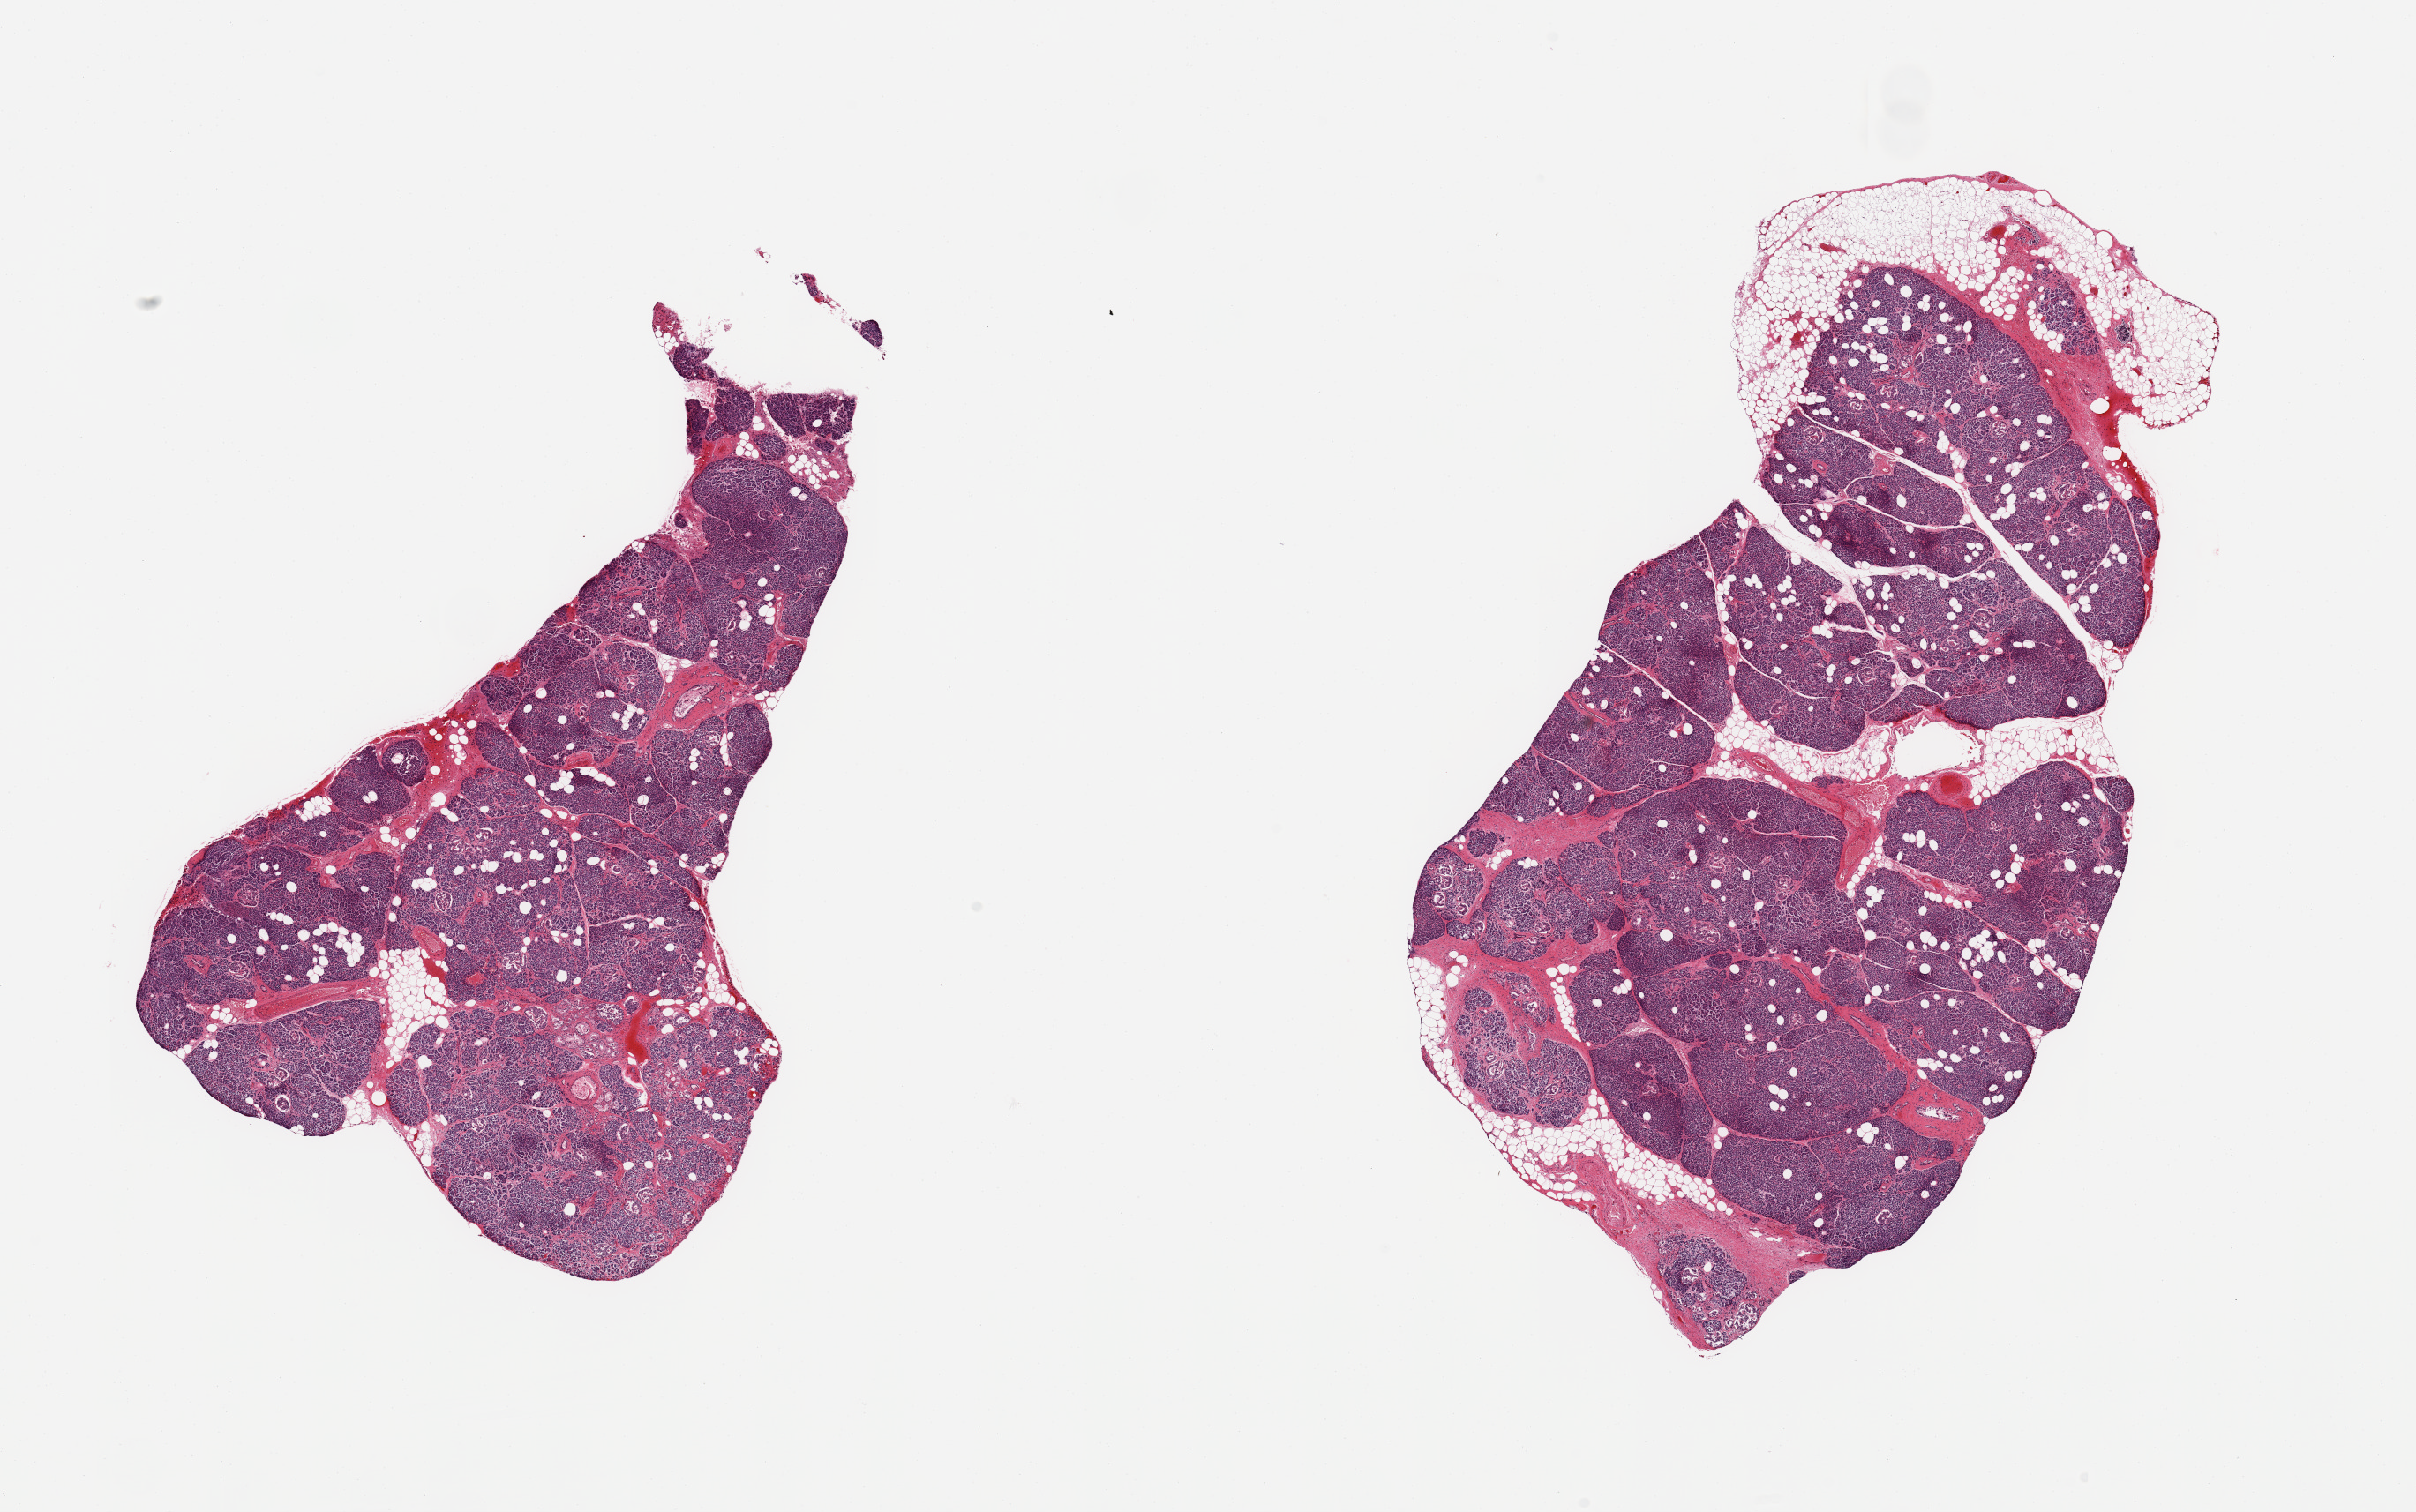
Haematoxylin and eosin whole-slide image — a low-resolution overview of the entire scanned area, about 21.7 x 13.6 mm. PAXgene-fixed, paraffin-embedded tissue. Sampled site (target tissue): pancreas. Donor tissue sample.
- pathologist's review note for this sample: 2 pieces; 1 piece includes ~10% attached fat, focal fibrosis/atrophy